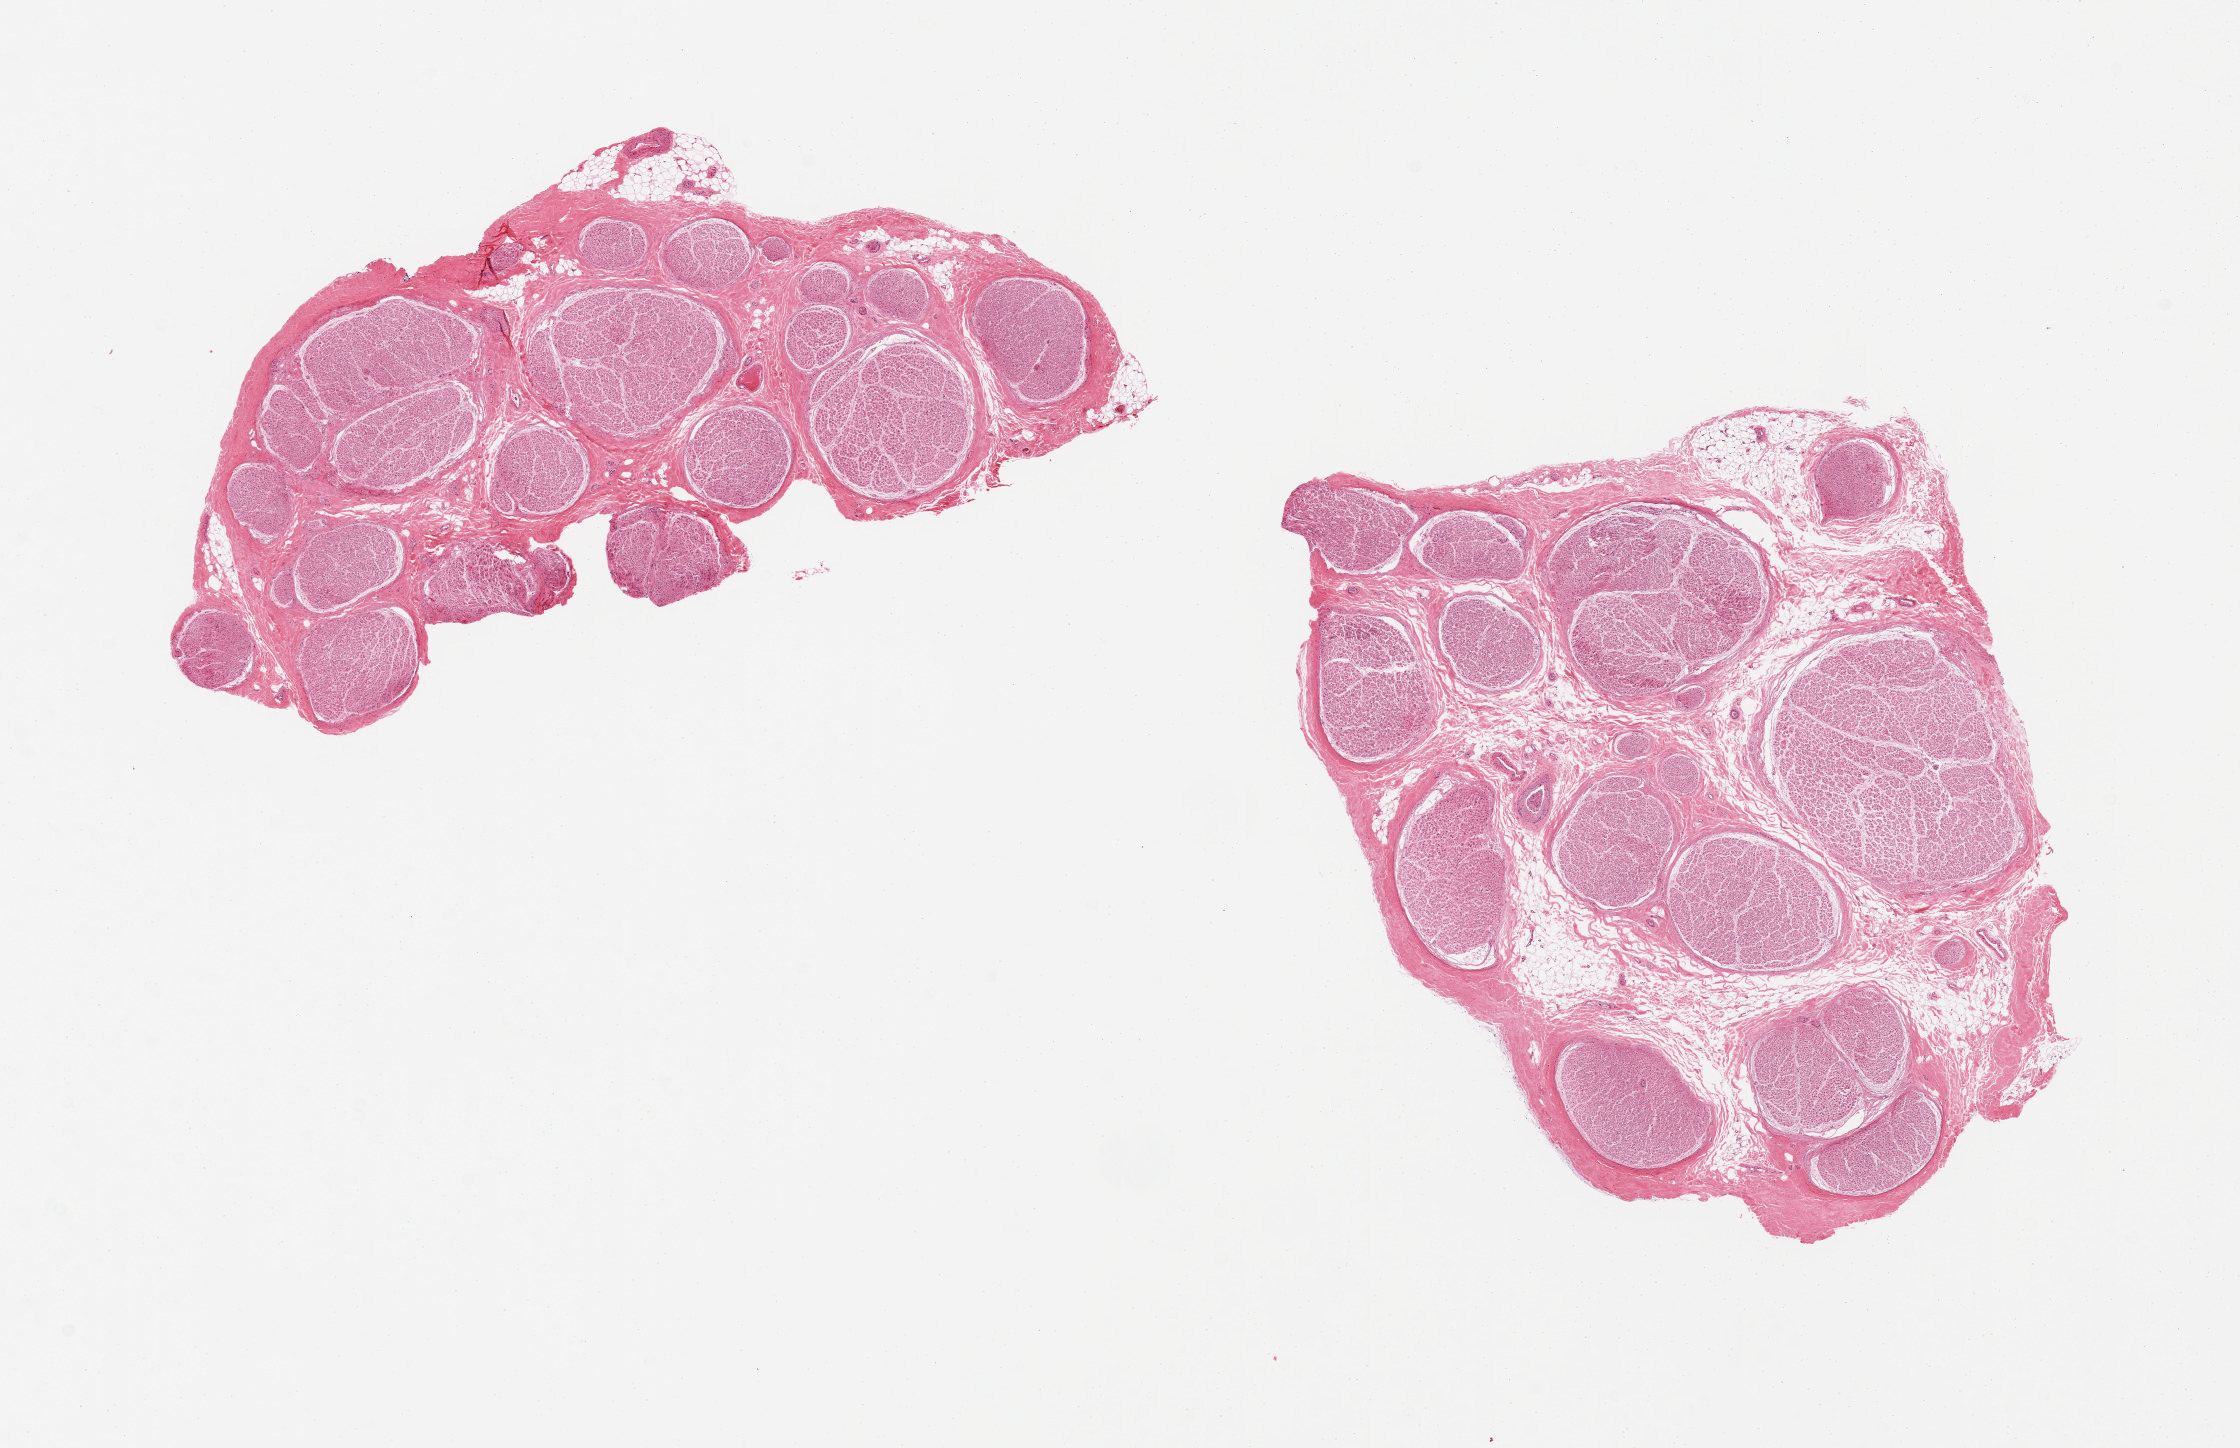
Hematoxylin and eosin (H&E) whole-slide image, low-resolution overview of the scanned area, about 17.7 x 11.5 mm (from a 20x scan), PAXgene-fixed, paraffin-embedded tissue, section of tibial nerve (target tissue), donor tissue sample.
Reviewer comment on this tissue sample: 2 pieces, minimal adherent fat, clean specimens.